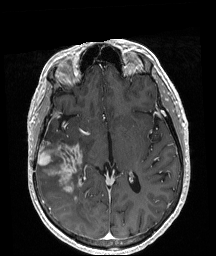
Brain MRI from a brain-tumour surgery series, one axial slice; slice 106 of 208 in the series (ordered by position); T1-weighted post-contrast; 1 mm slice thickness; 216 × 256 image matrix, field of view 211 × 250 mm. Case-level facts recorded for this patient, not image findings: histopathology: Astrocytoma; WHO grade: 4; IDH mutation: yes; tumour location: Right Temporal.
Structures marked on this image (expert manual segmentation):
- tumour: box from (x=38, y=143) to (x=82, y=193) px